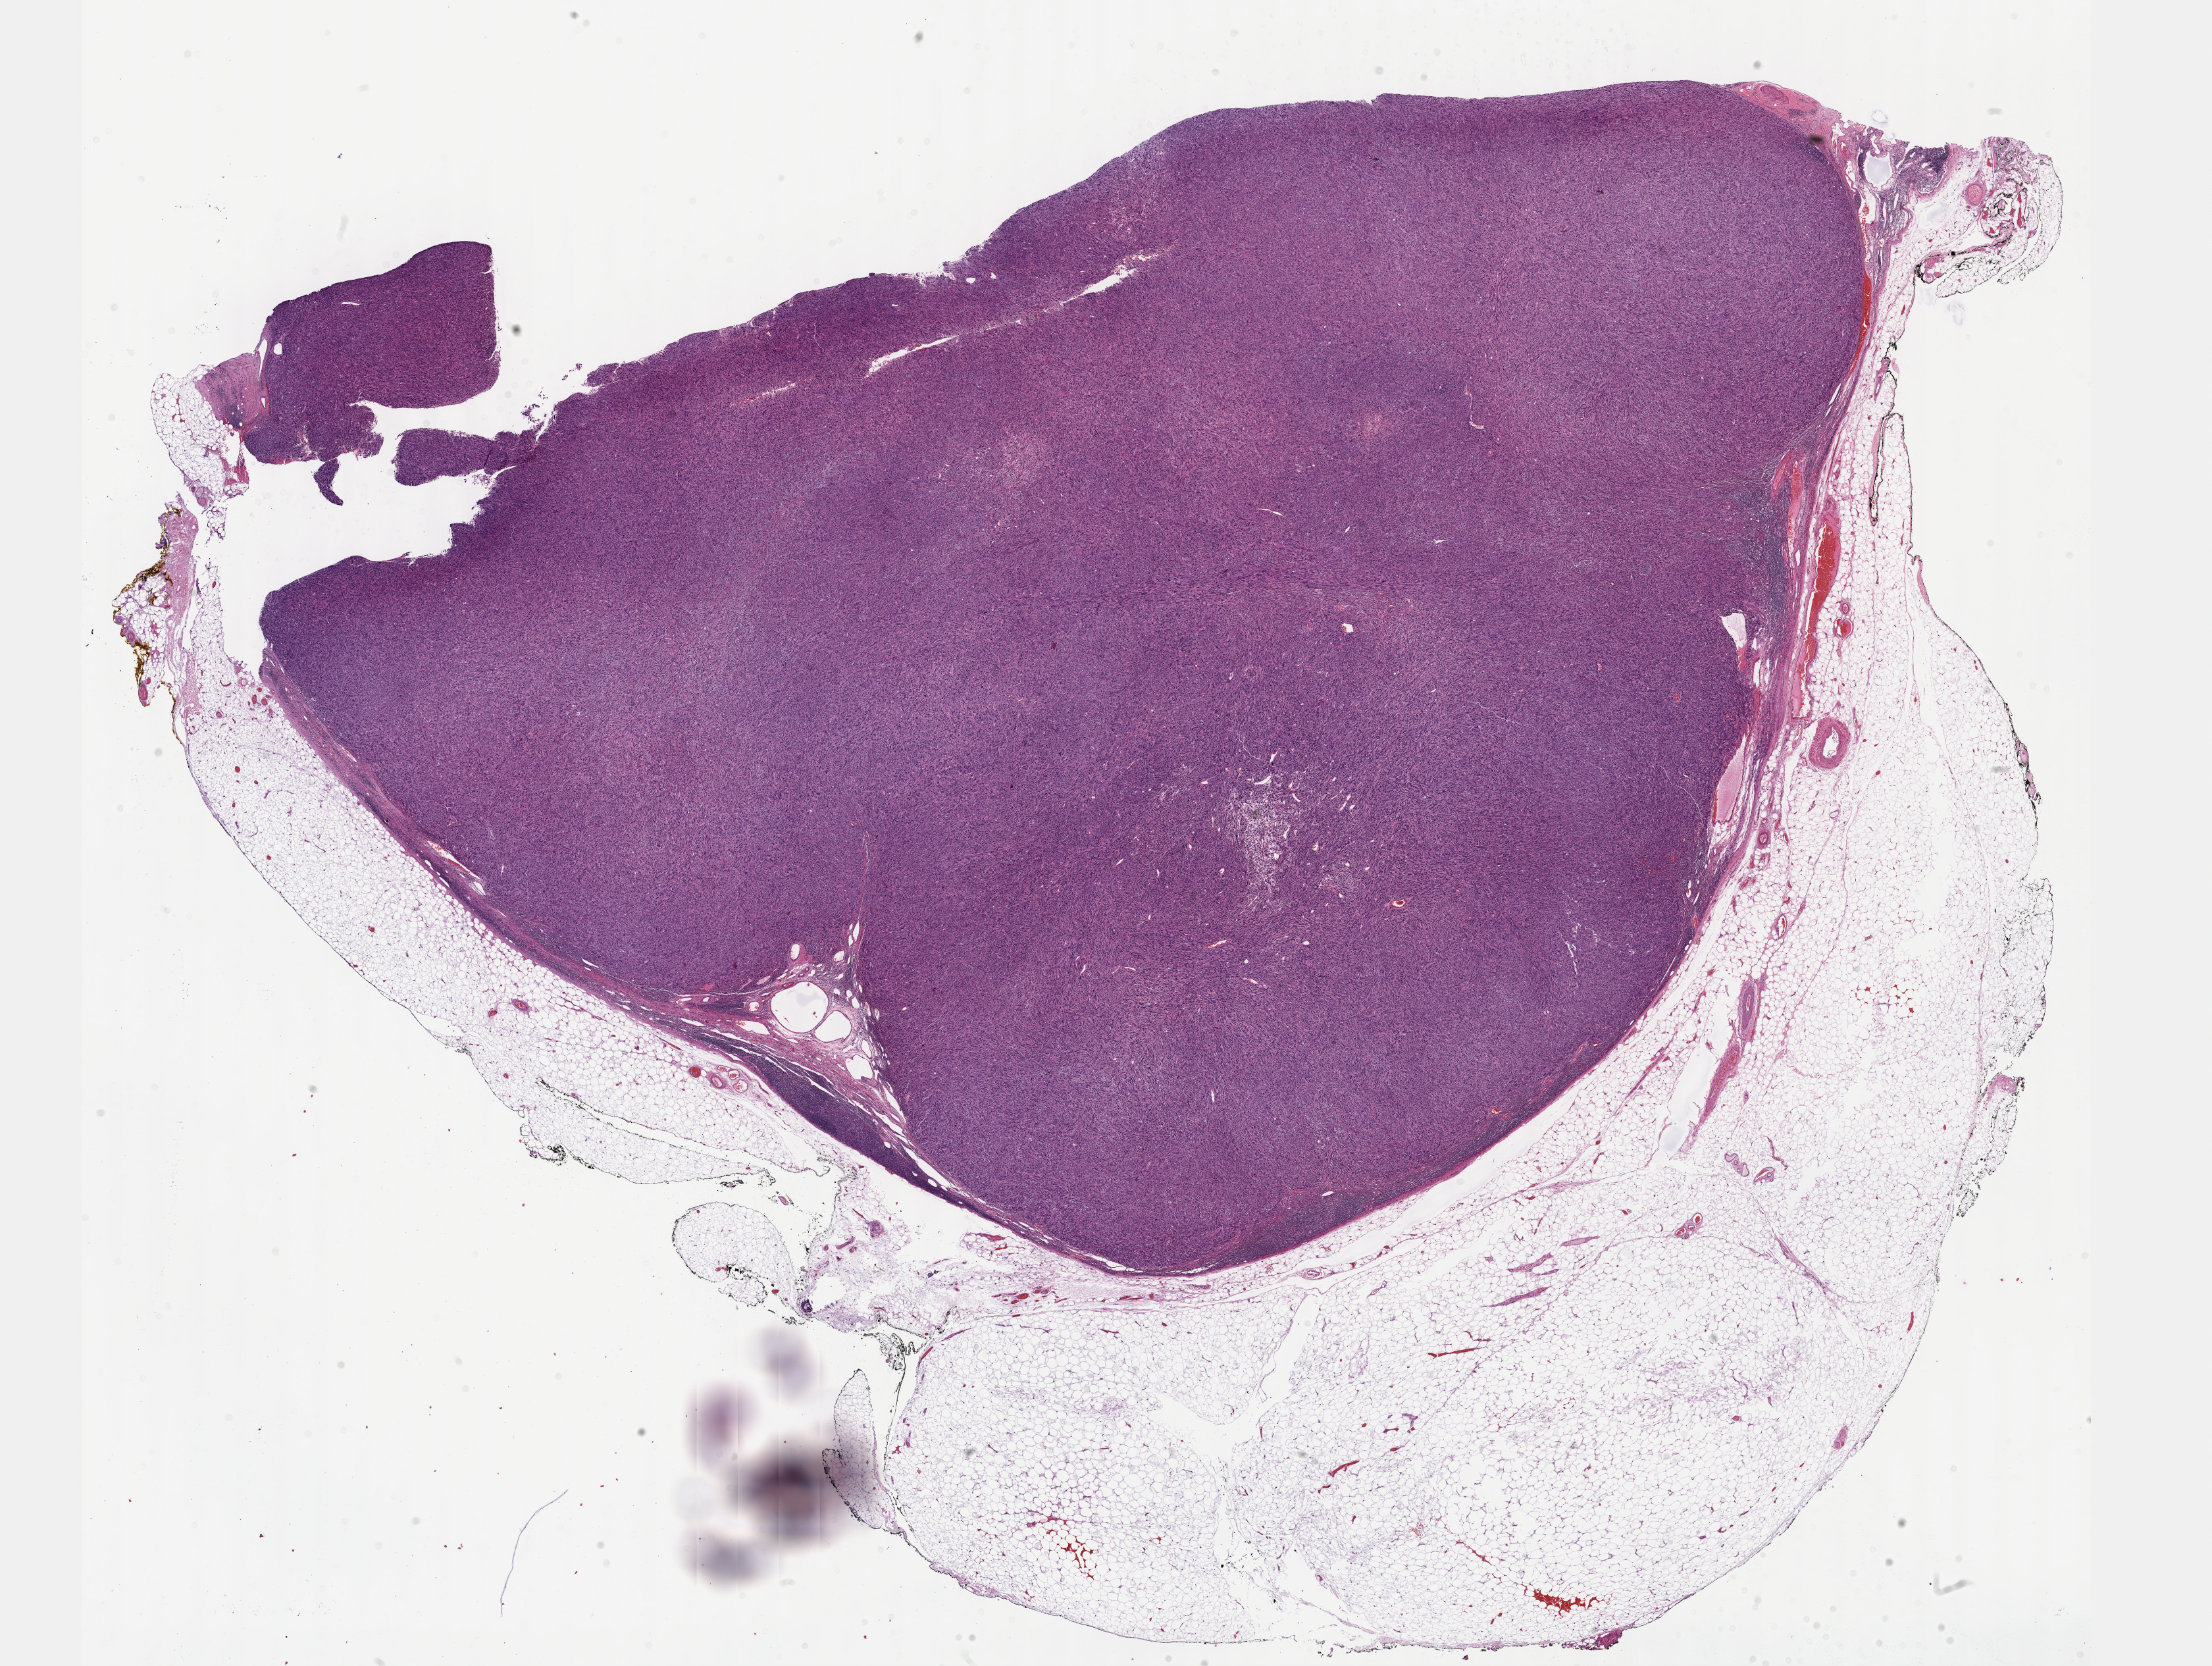
Digitized H&E tissue section (whole slide) — a low-resolution overview of the entire scanned area, about 27.2 x 20.5 mm (acquisition: 40x scan). Formalin-fixed paraffin-embedded (FFPE) diagnostic section. Connective, subcutaneous and other soft tissues, primary tumour sample. Patient: female, age at initial diagnosis 49 years.
Pathologic diagnosis: Undifferentiated sarcoma (connective, subcutaneous and other soft tissues of lower limb and hip).